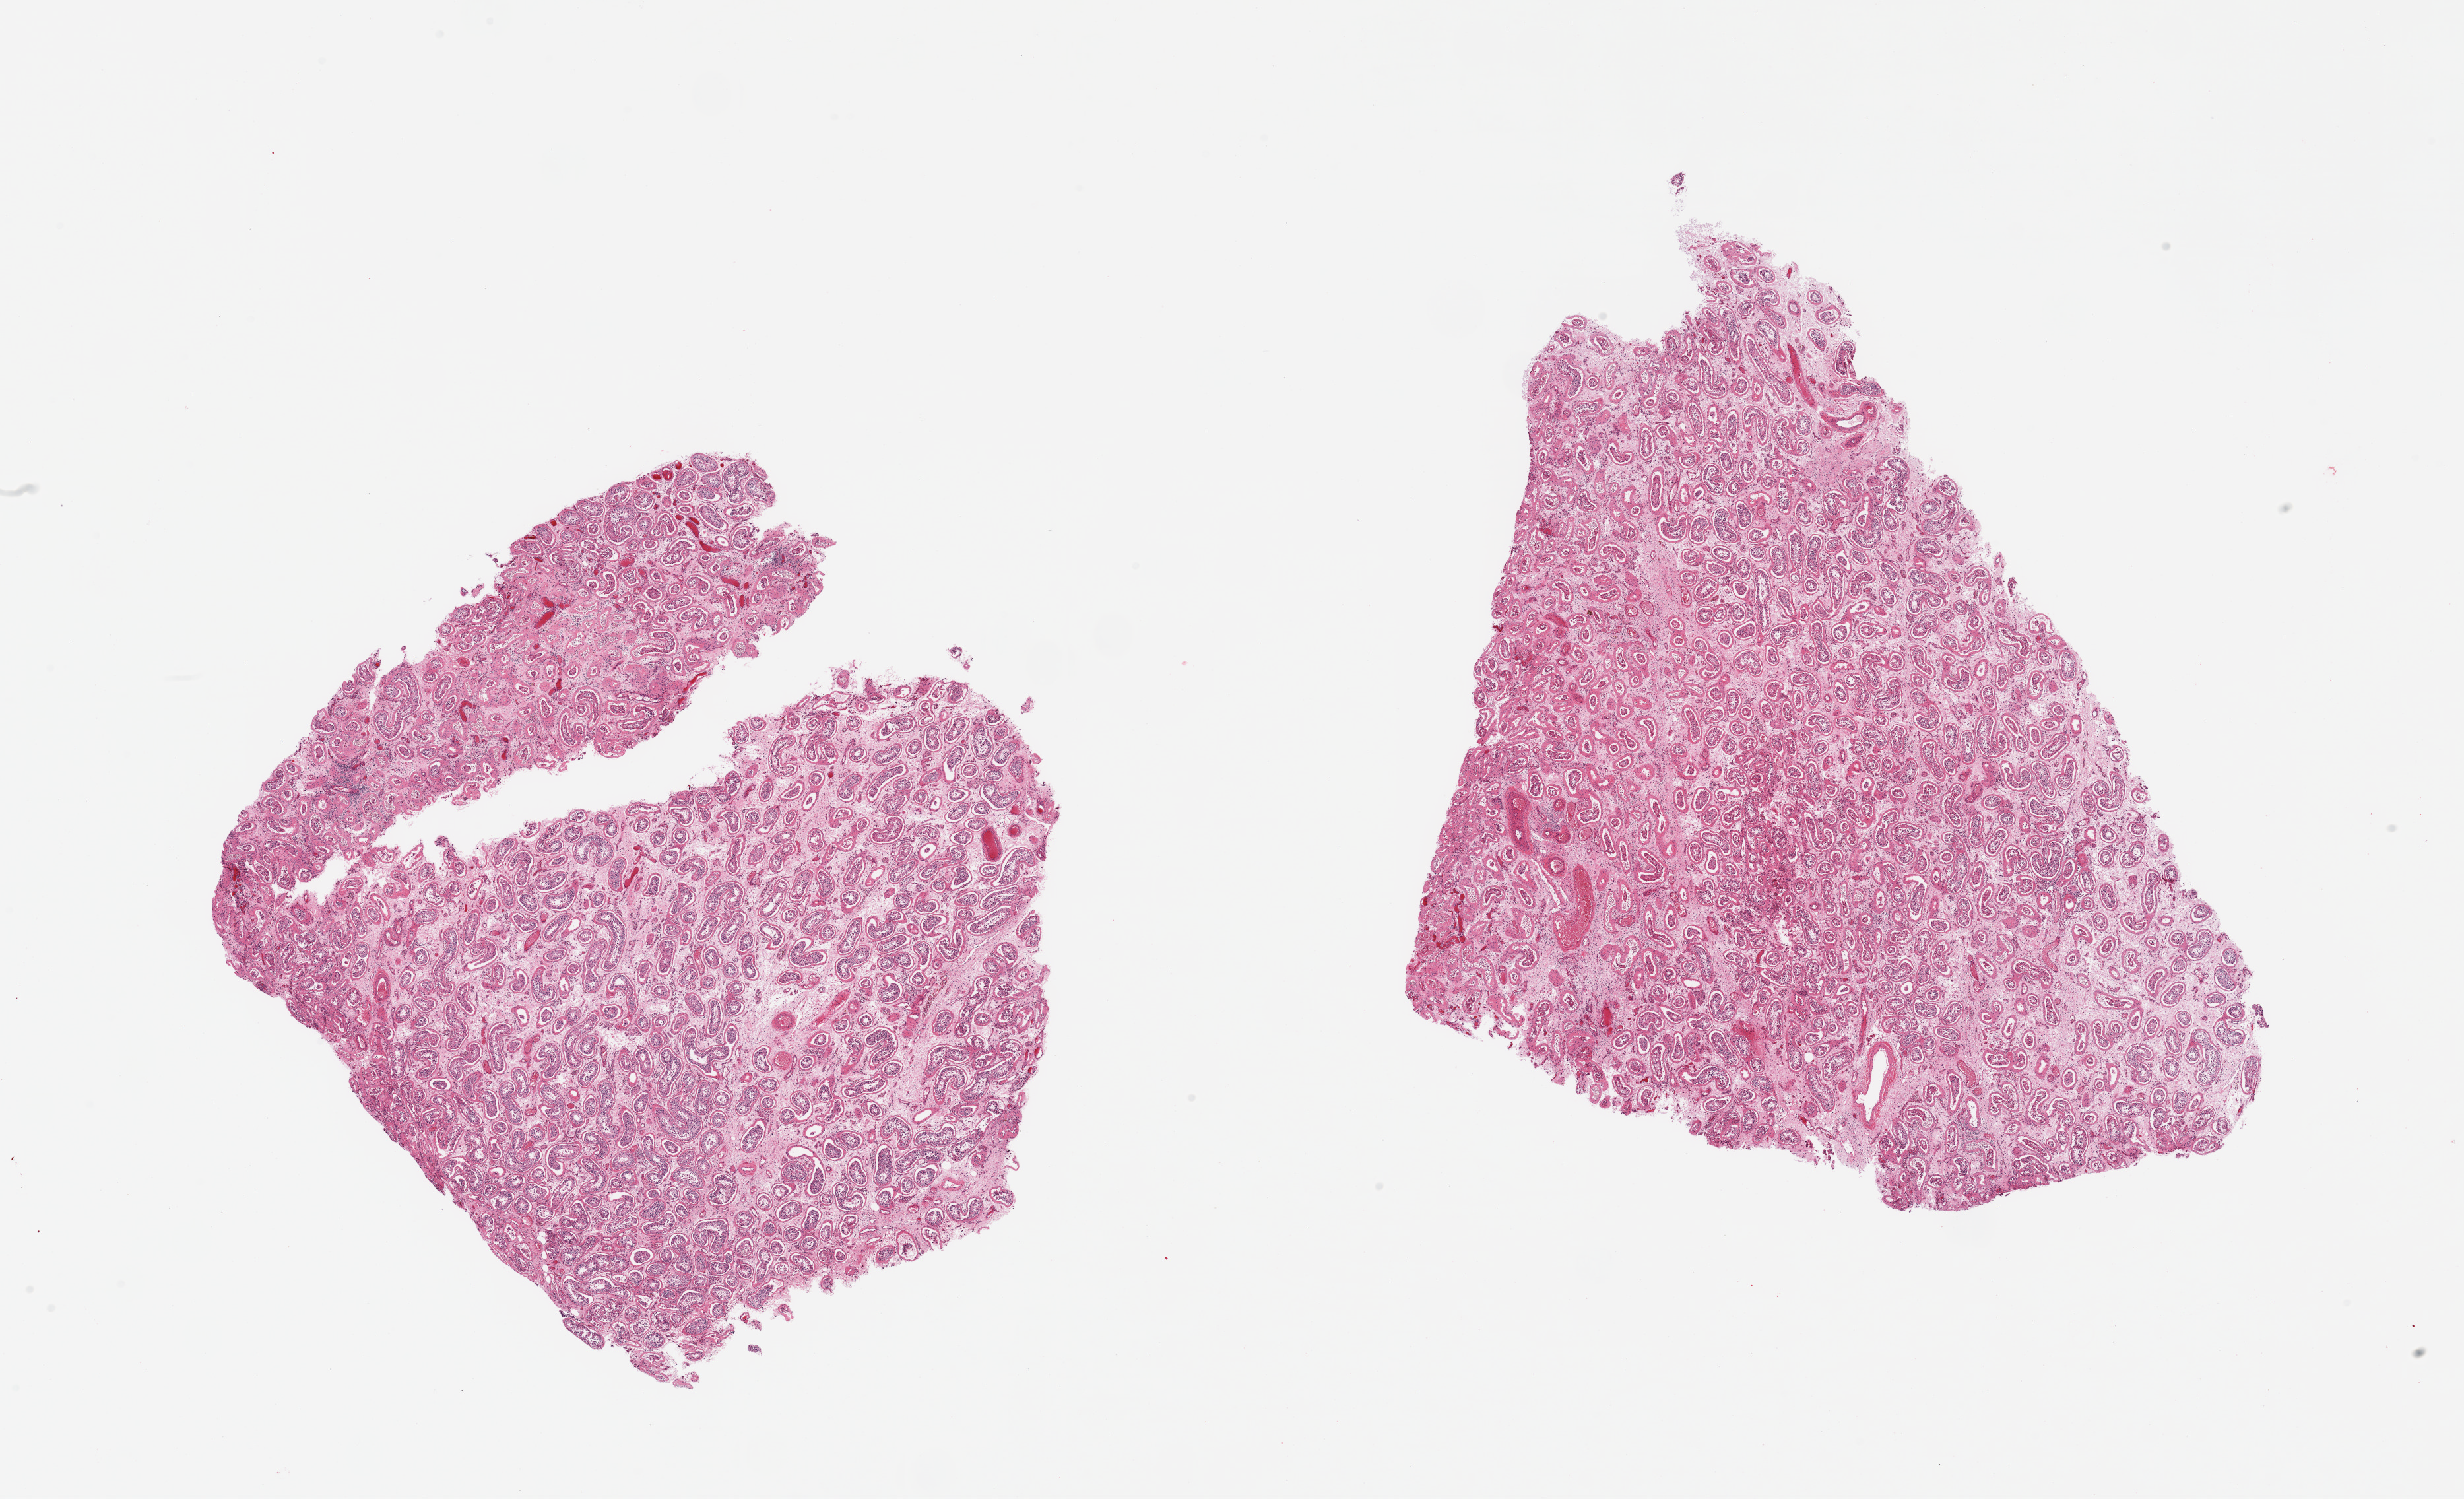
Digitized H&E-stained section, a low-resolution overview of the entire scanned area, about 29.5 x 18.0 mm (slide scanned at 20x), PAXgene-fixed, paraffin-embedded tissue, sampled site (target tissue): testis, donor tissue sample. Donor: male.
Pathologist's review note for this sample: 2 pieces; severely reduced mature spermatogenesis.